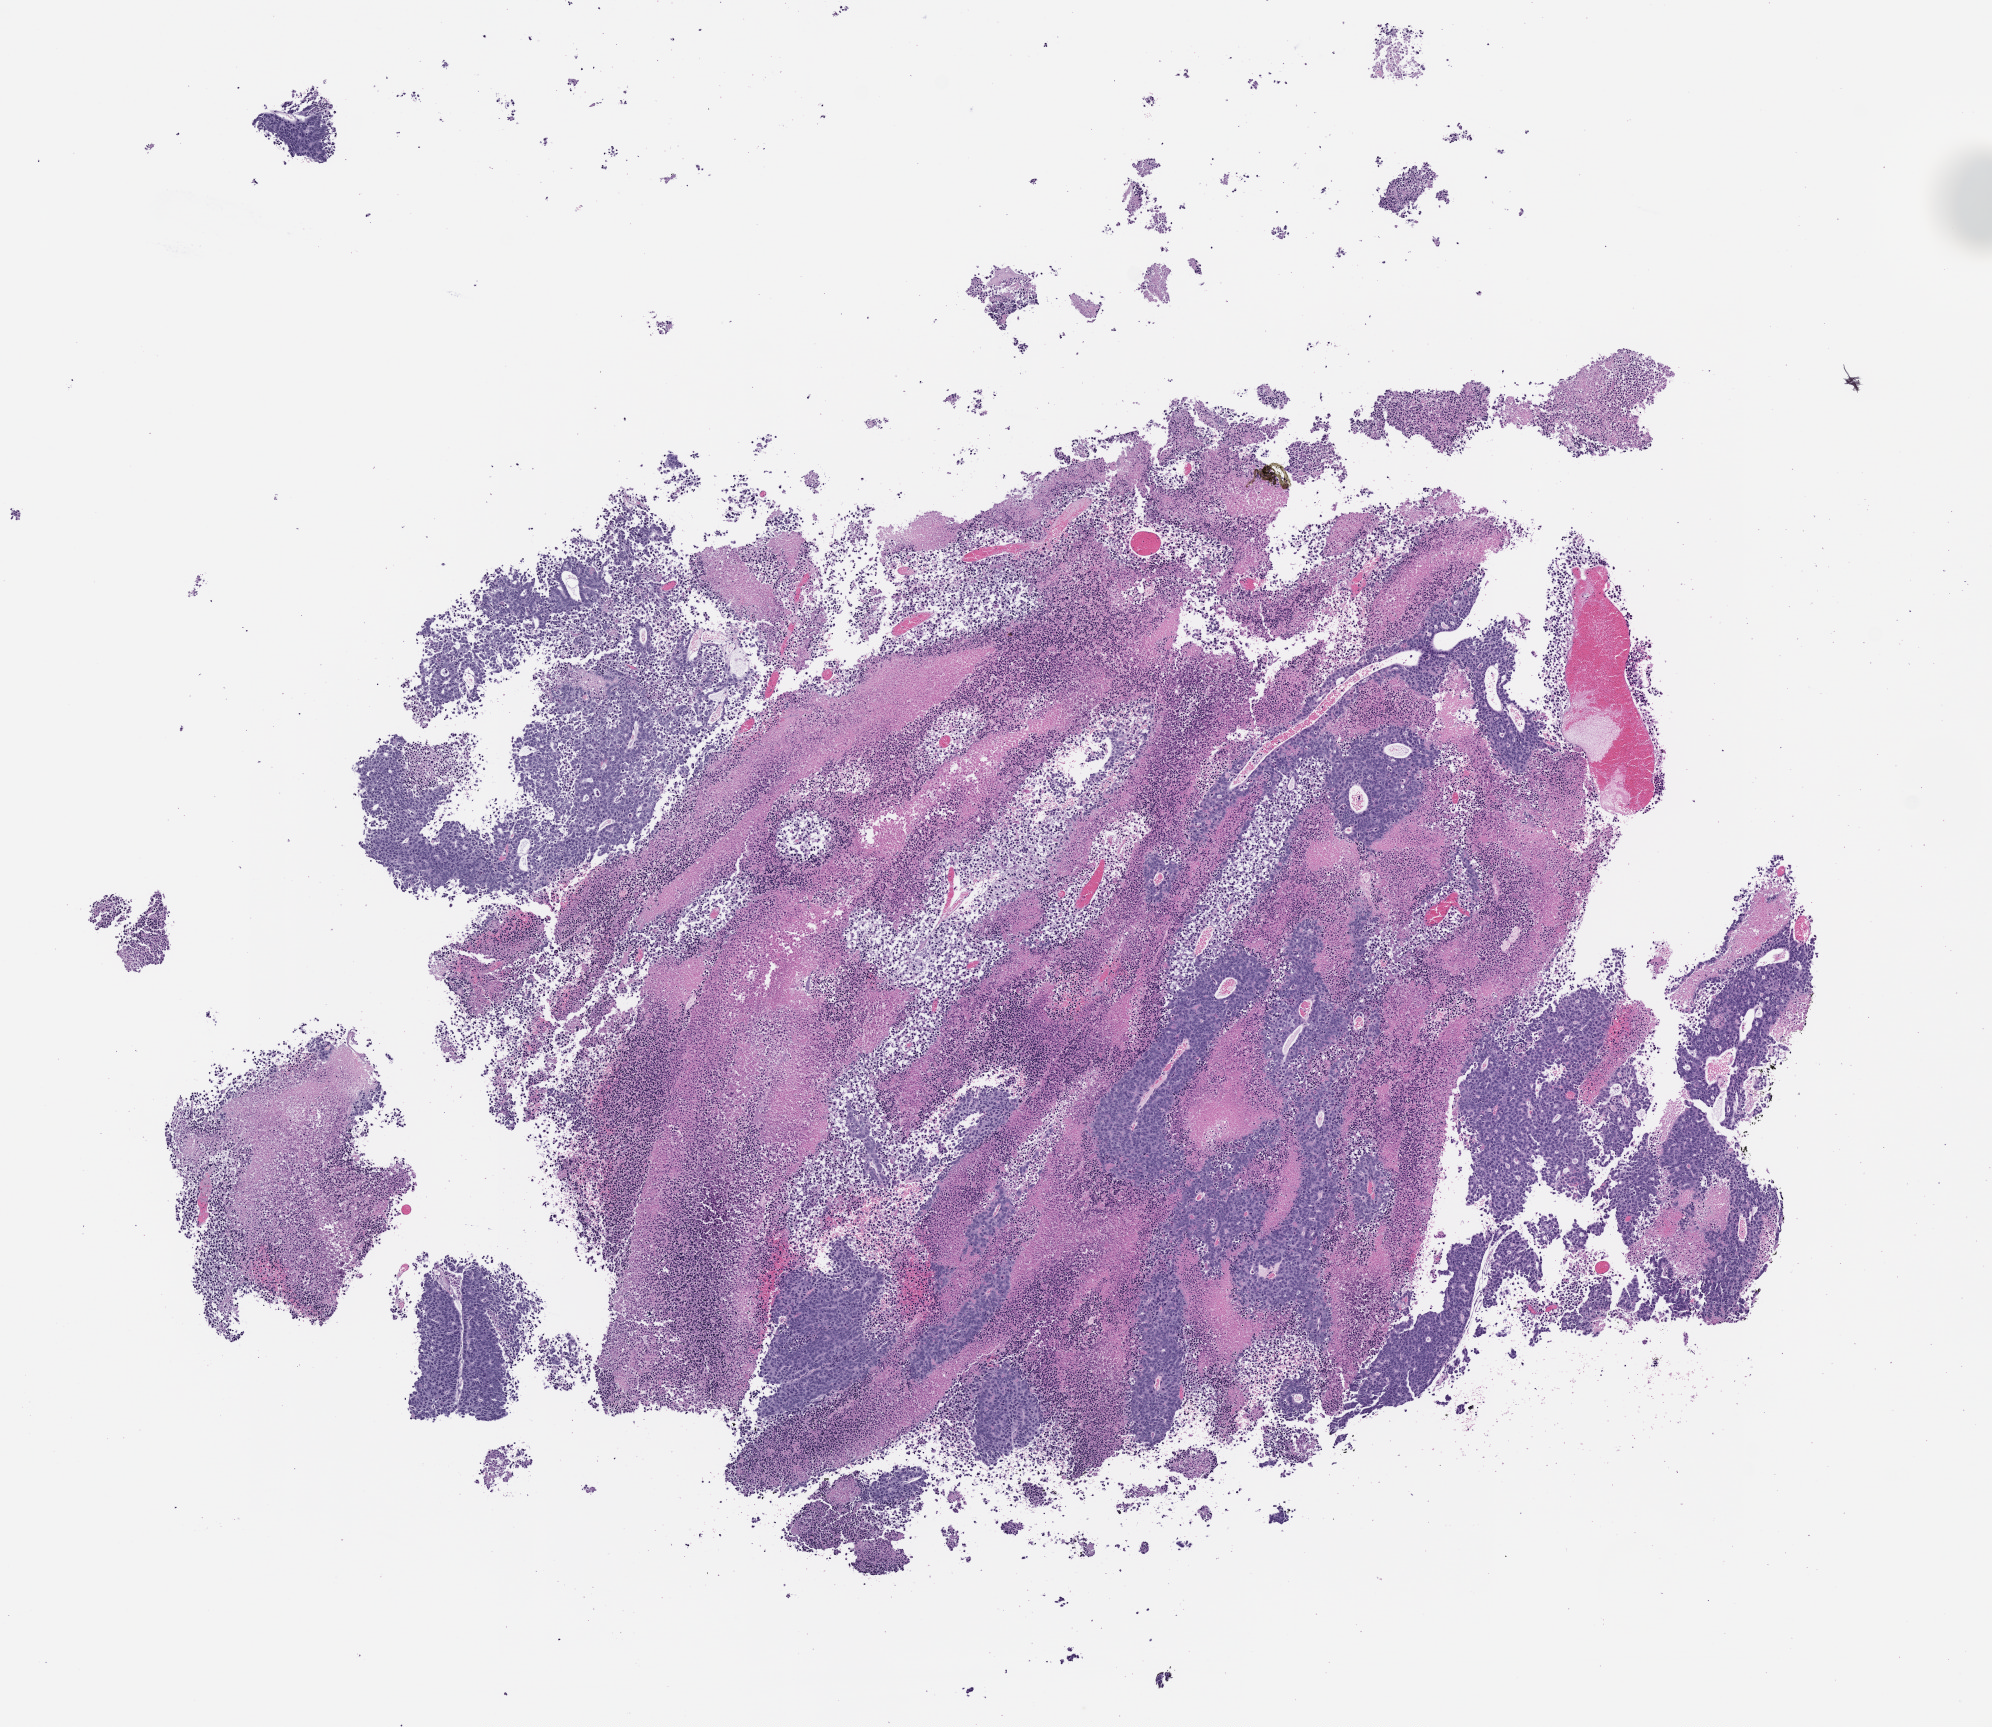
Whole-slide image, H&E: patient-derived xenograft (human tumor grown in a mouse), passage 2, a low-resolution overview of the entire scanned area, about 8.0 x 6.9 mm, formalin-fixed, paraffin-embedded (FFPE) tissue, tumor site category: colon.
Originating patient diagnosis: Colon Adenocarcinoma.